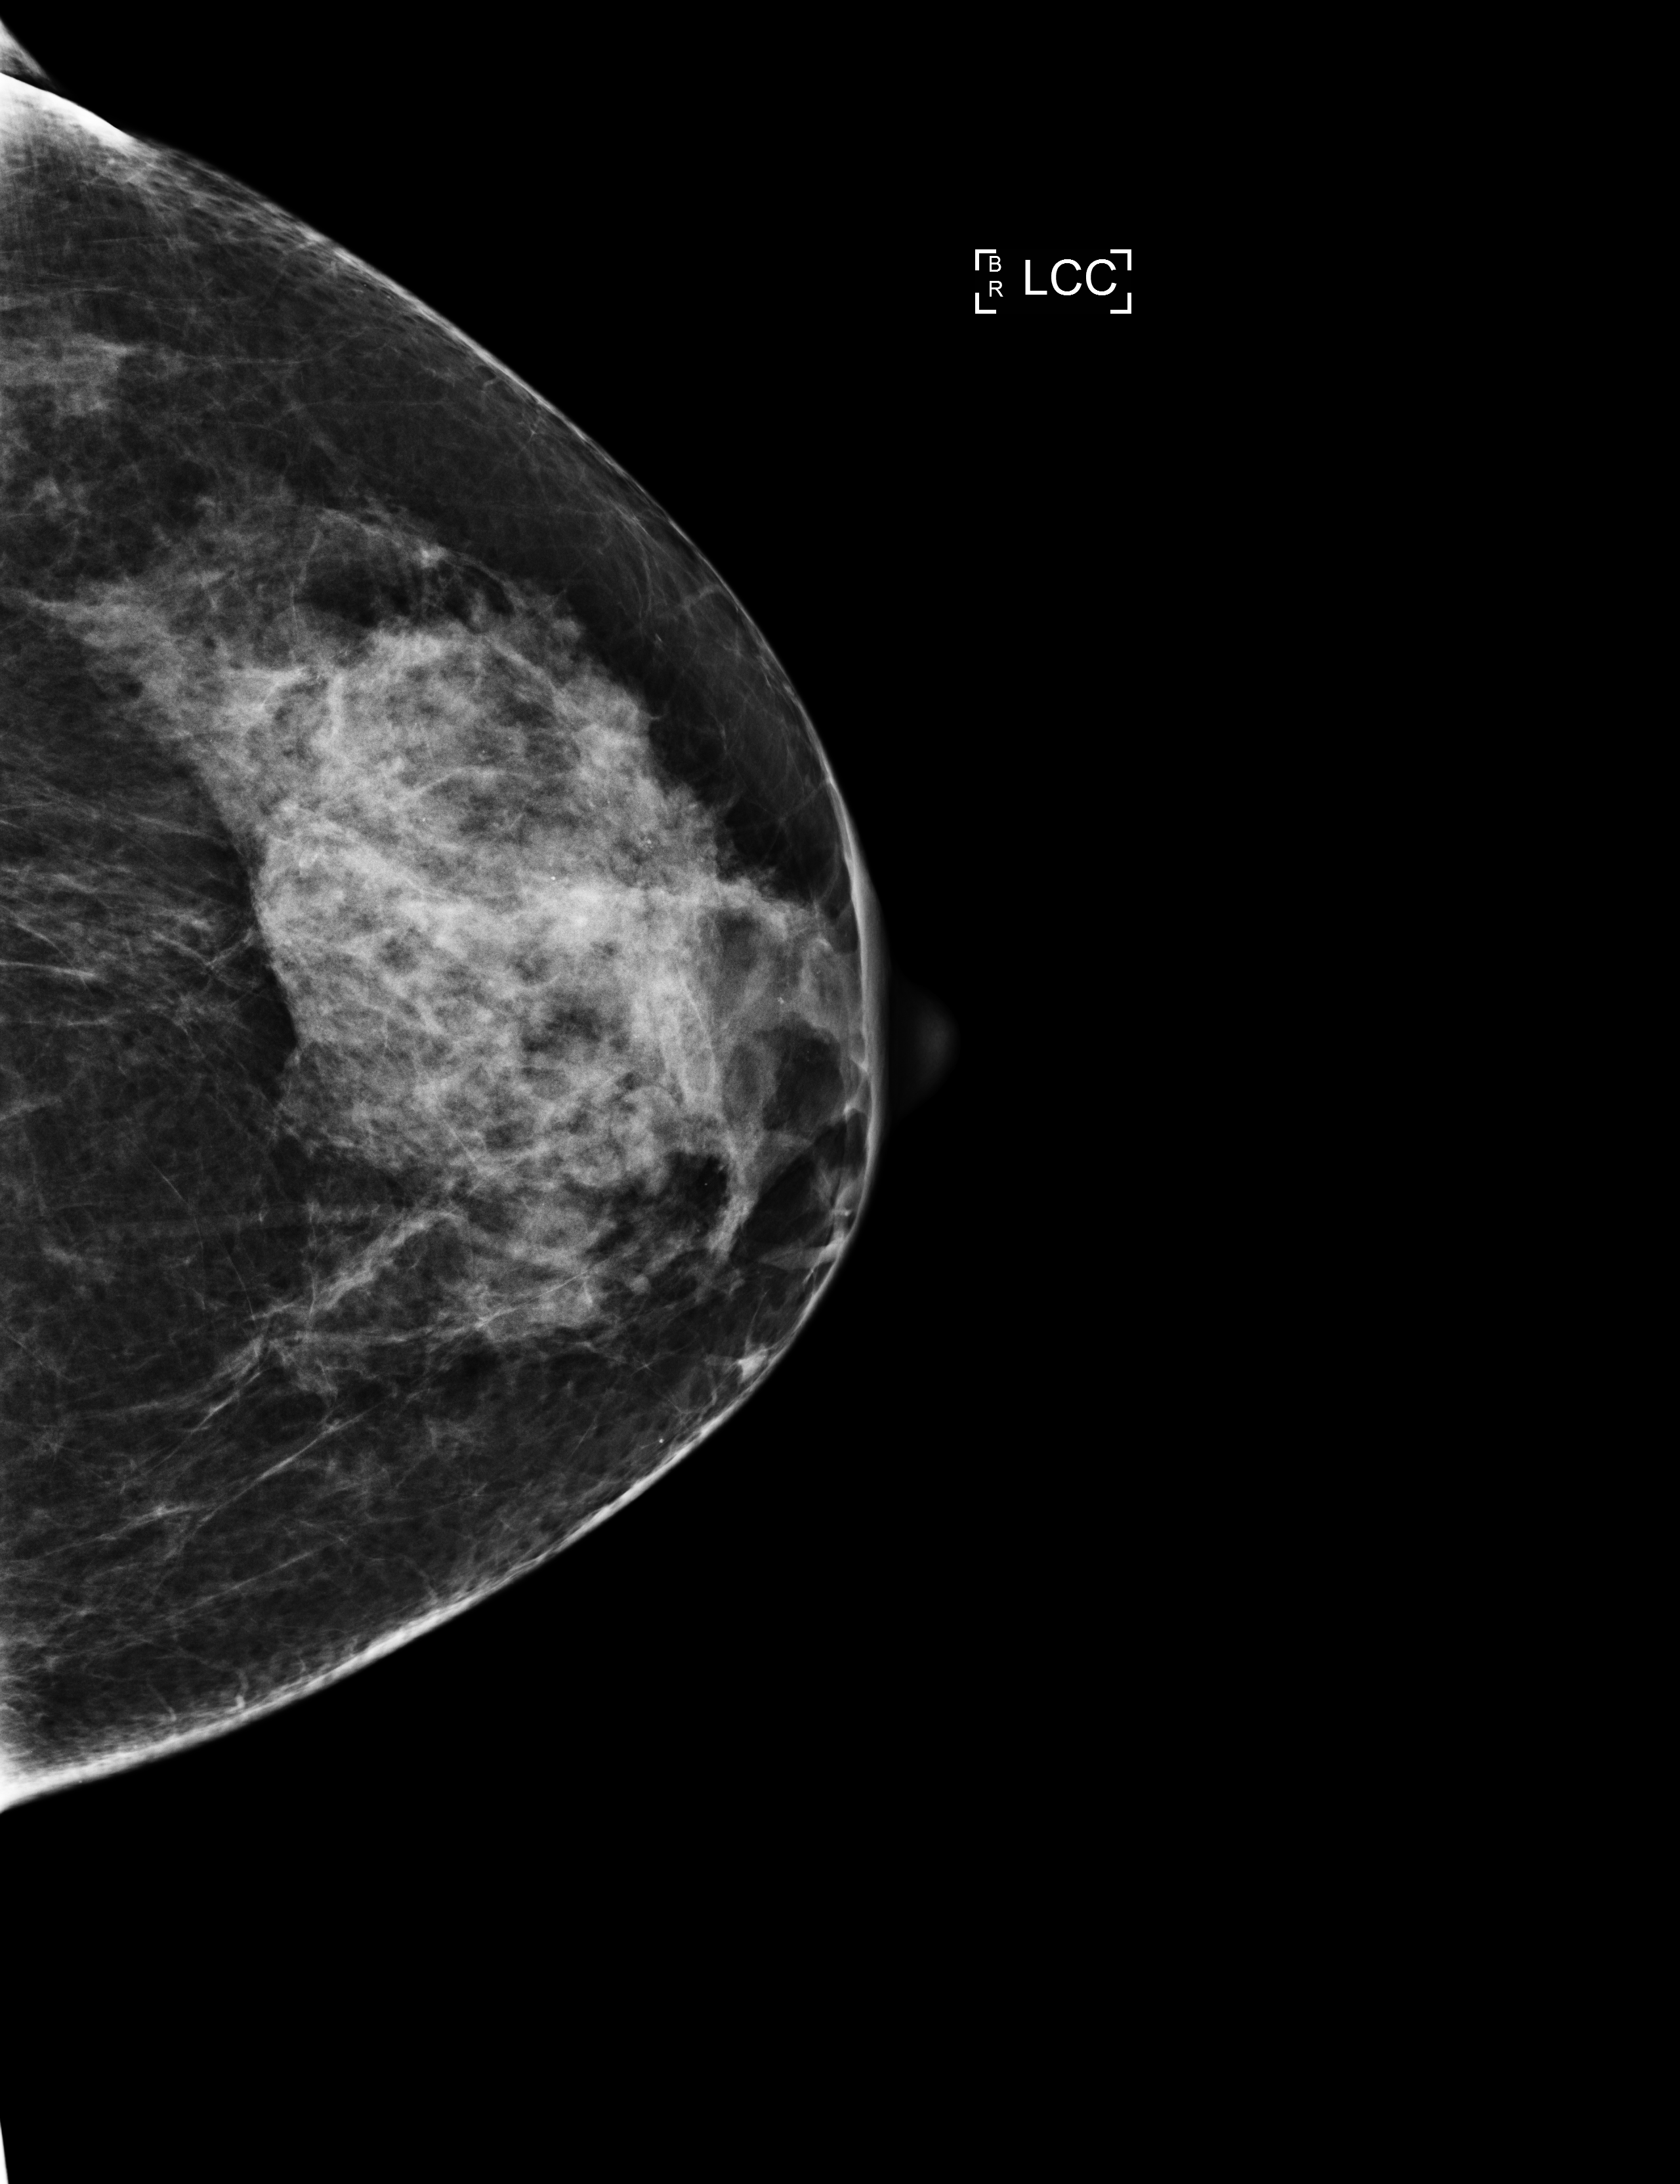
Screening examination. Patient: female, 56 years.
Image type: full-field digital mammogram. Breast: left. Projection: CC view.